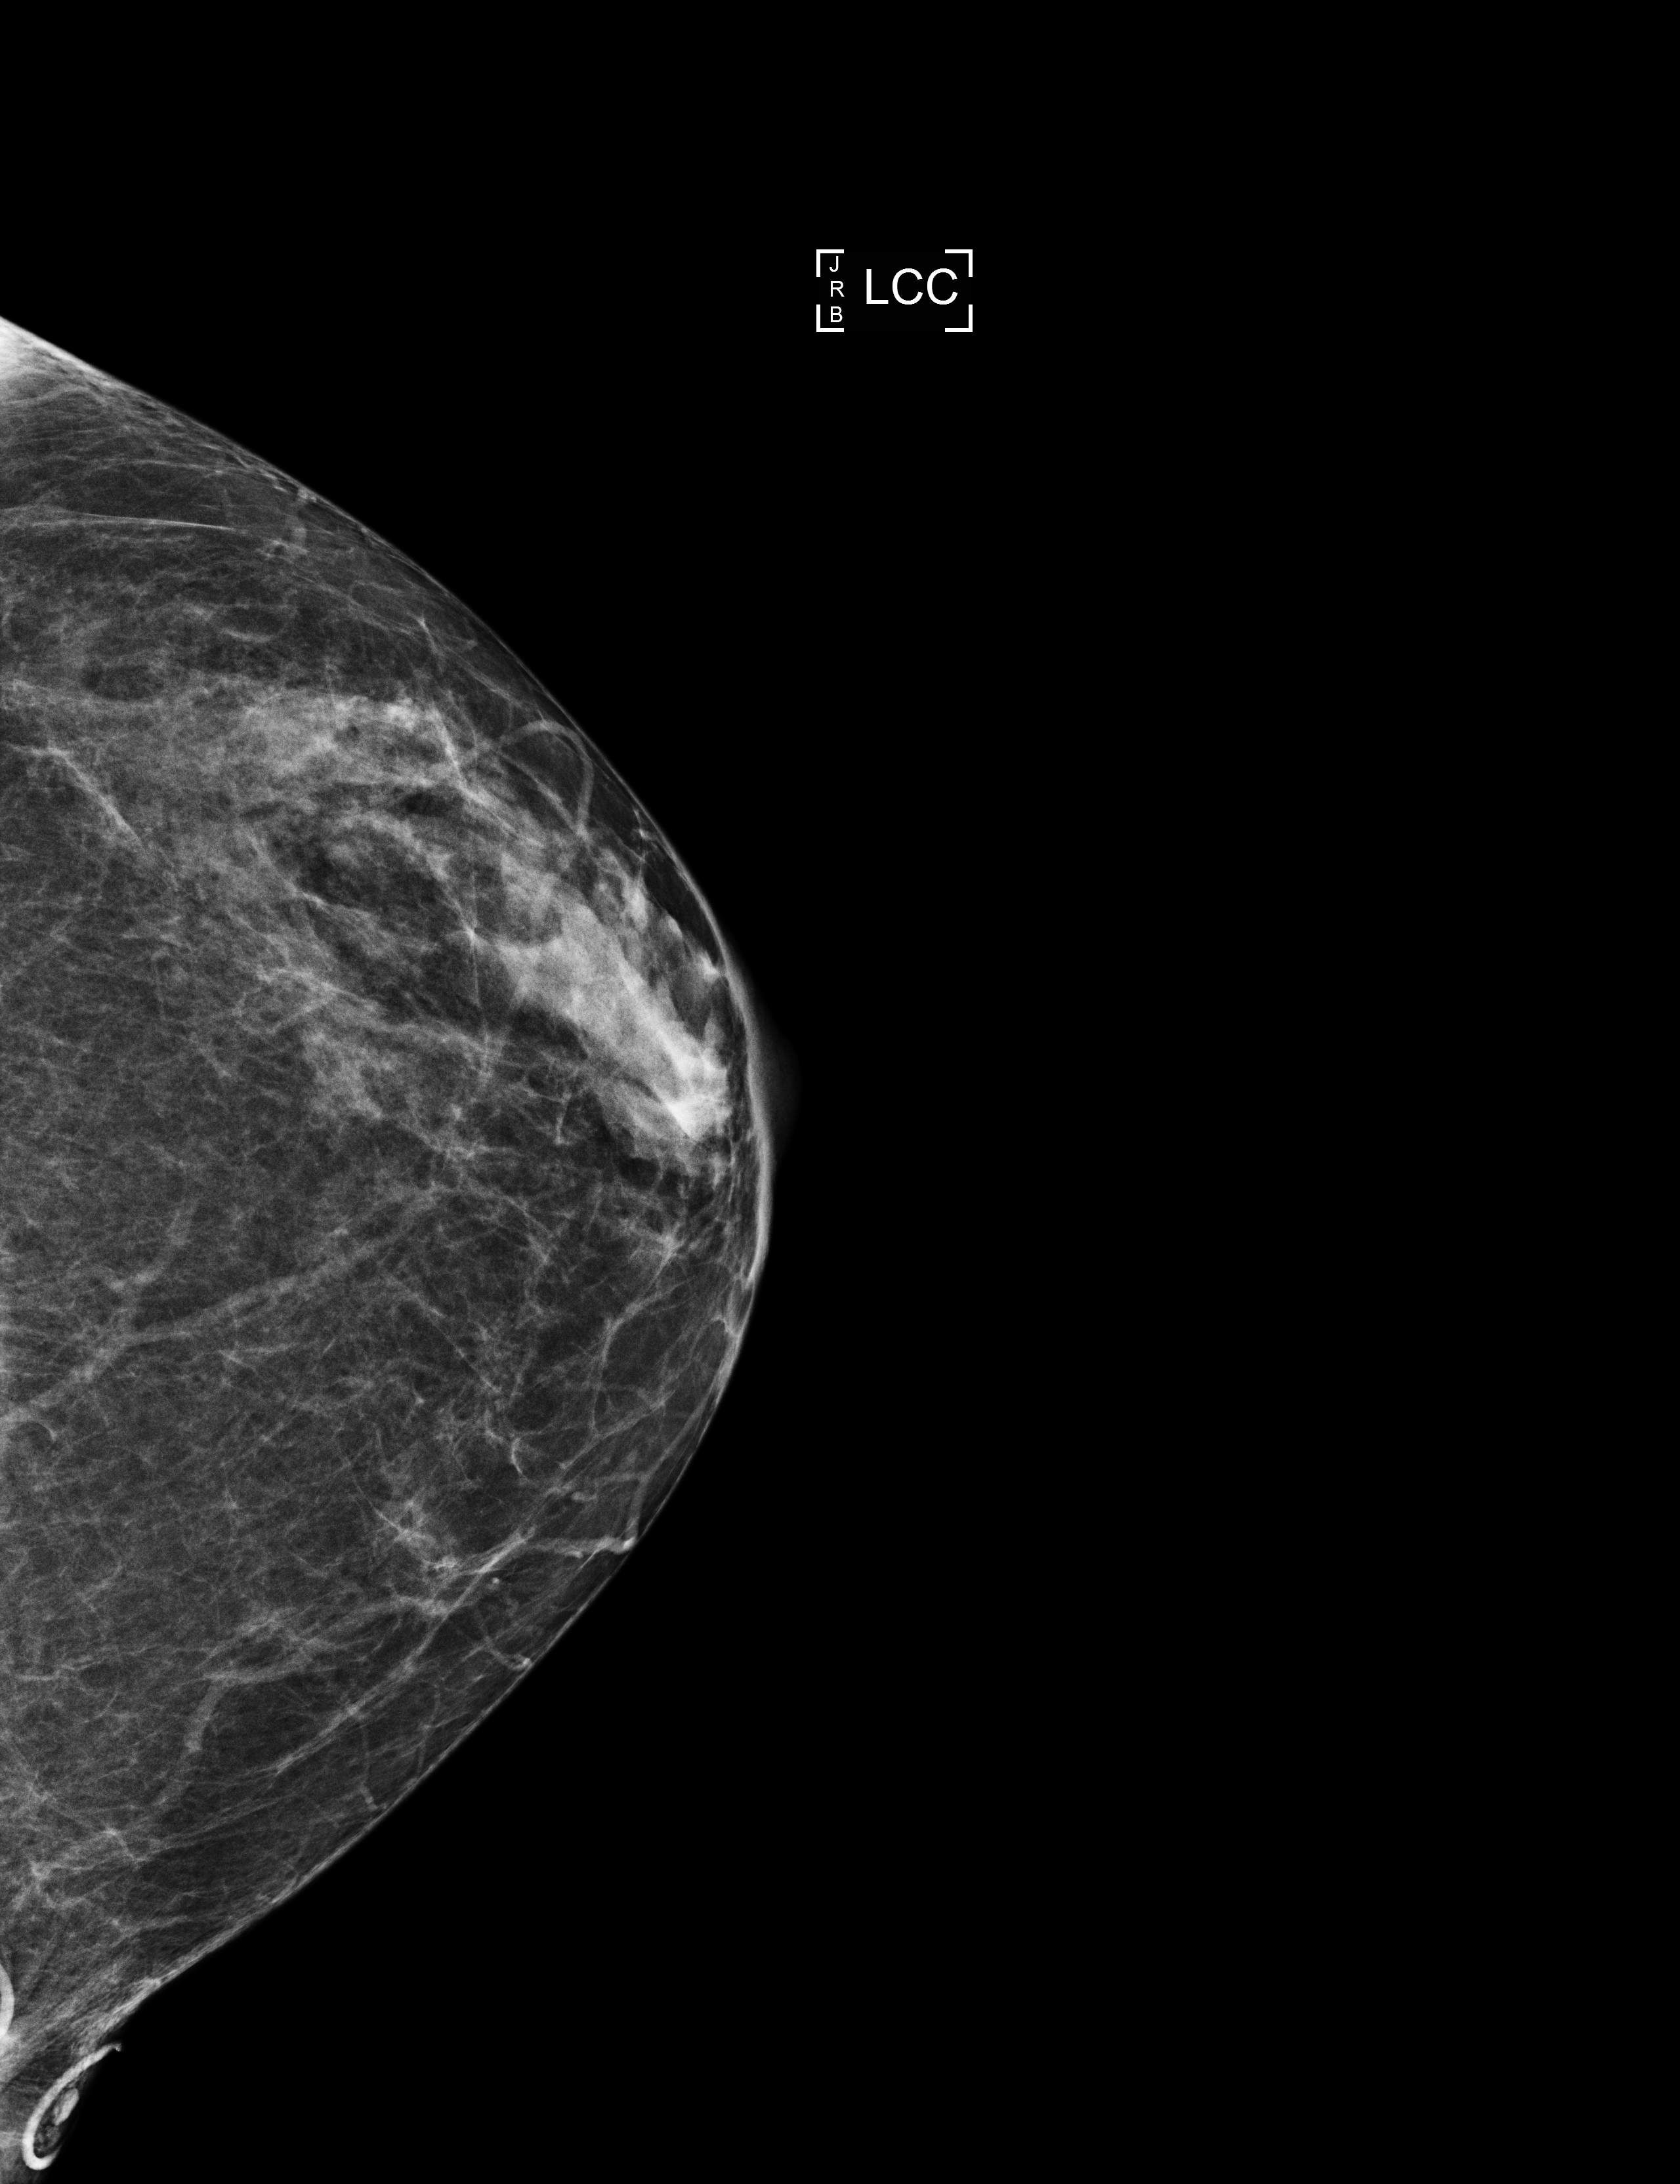
Screening examination. Female patient, age 60 years.
Image type: full-field digital mammogram. Breast: left. Projection: CC view.